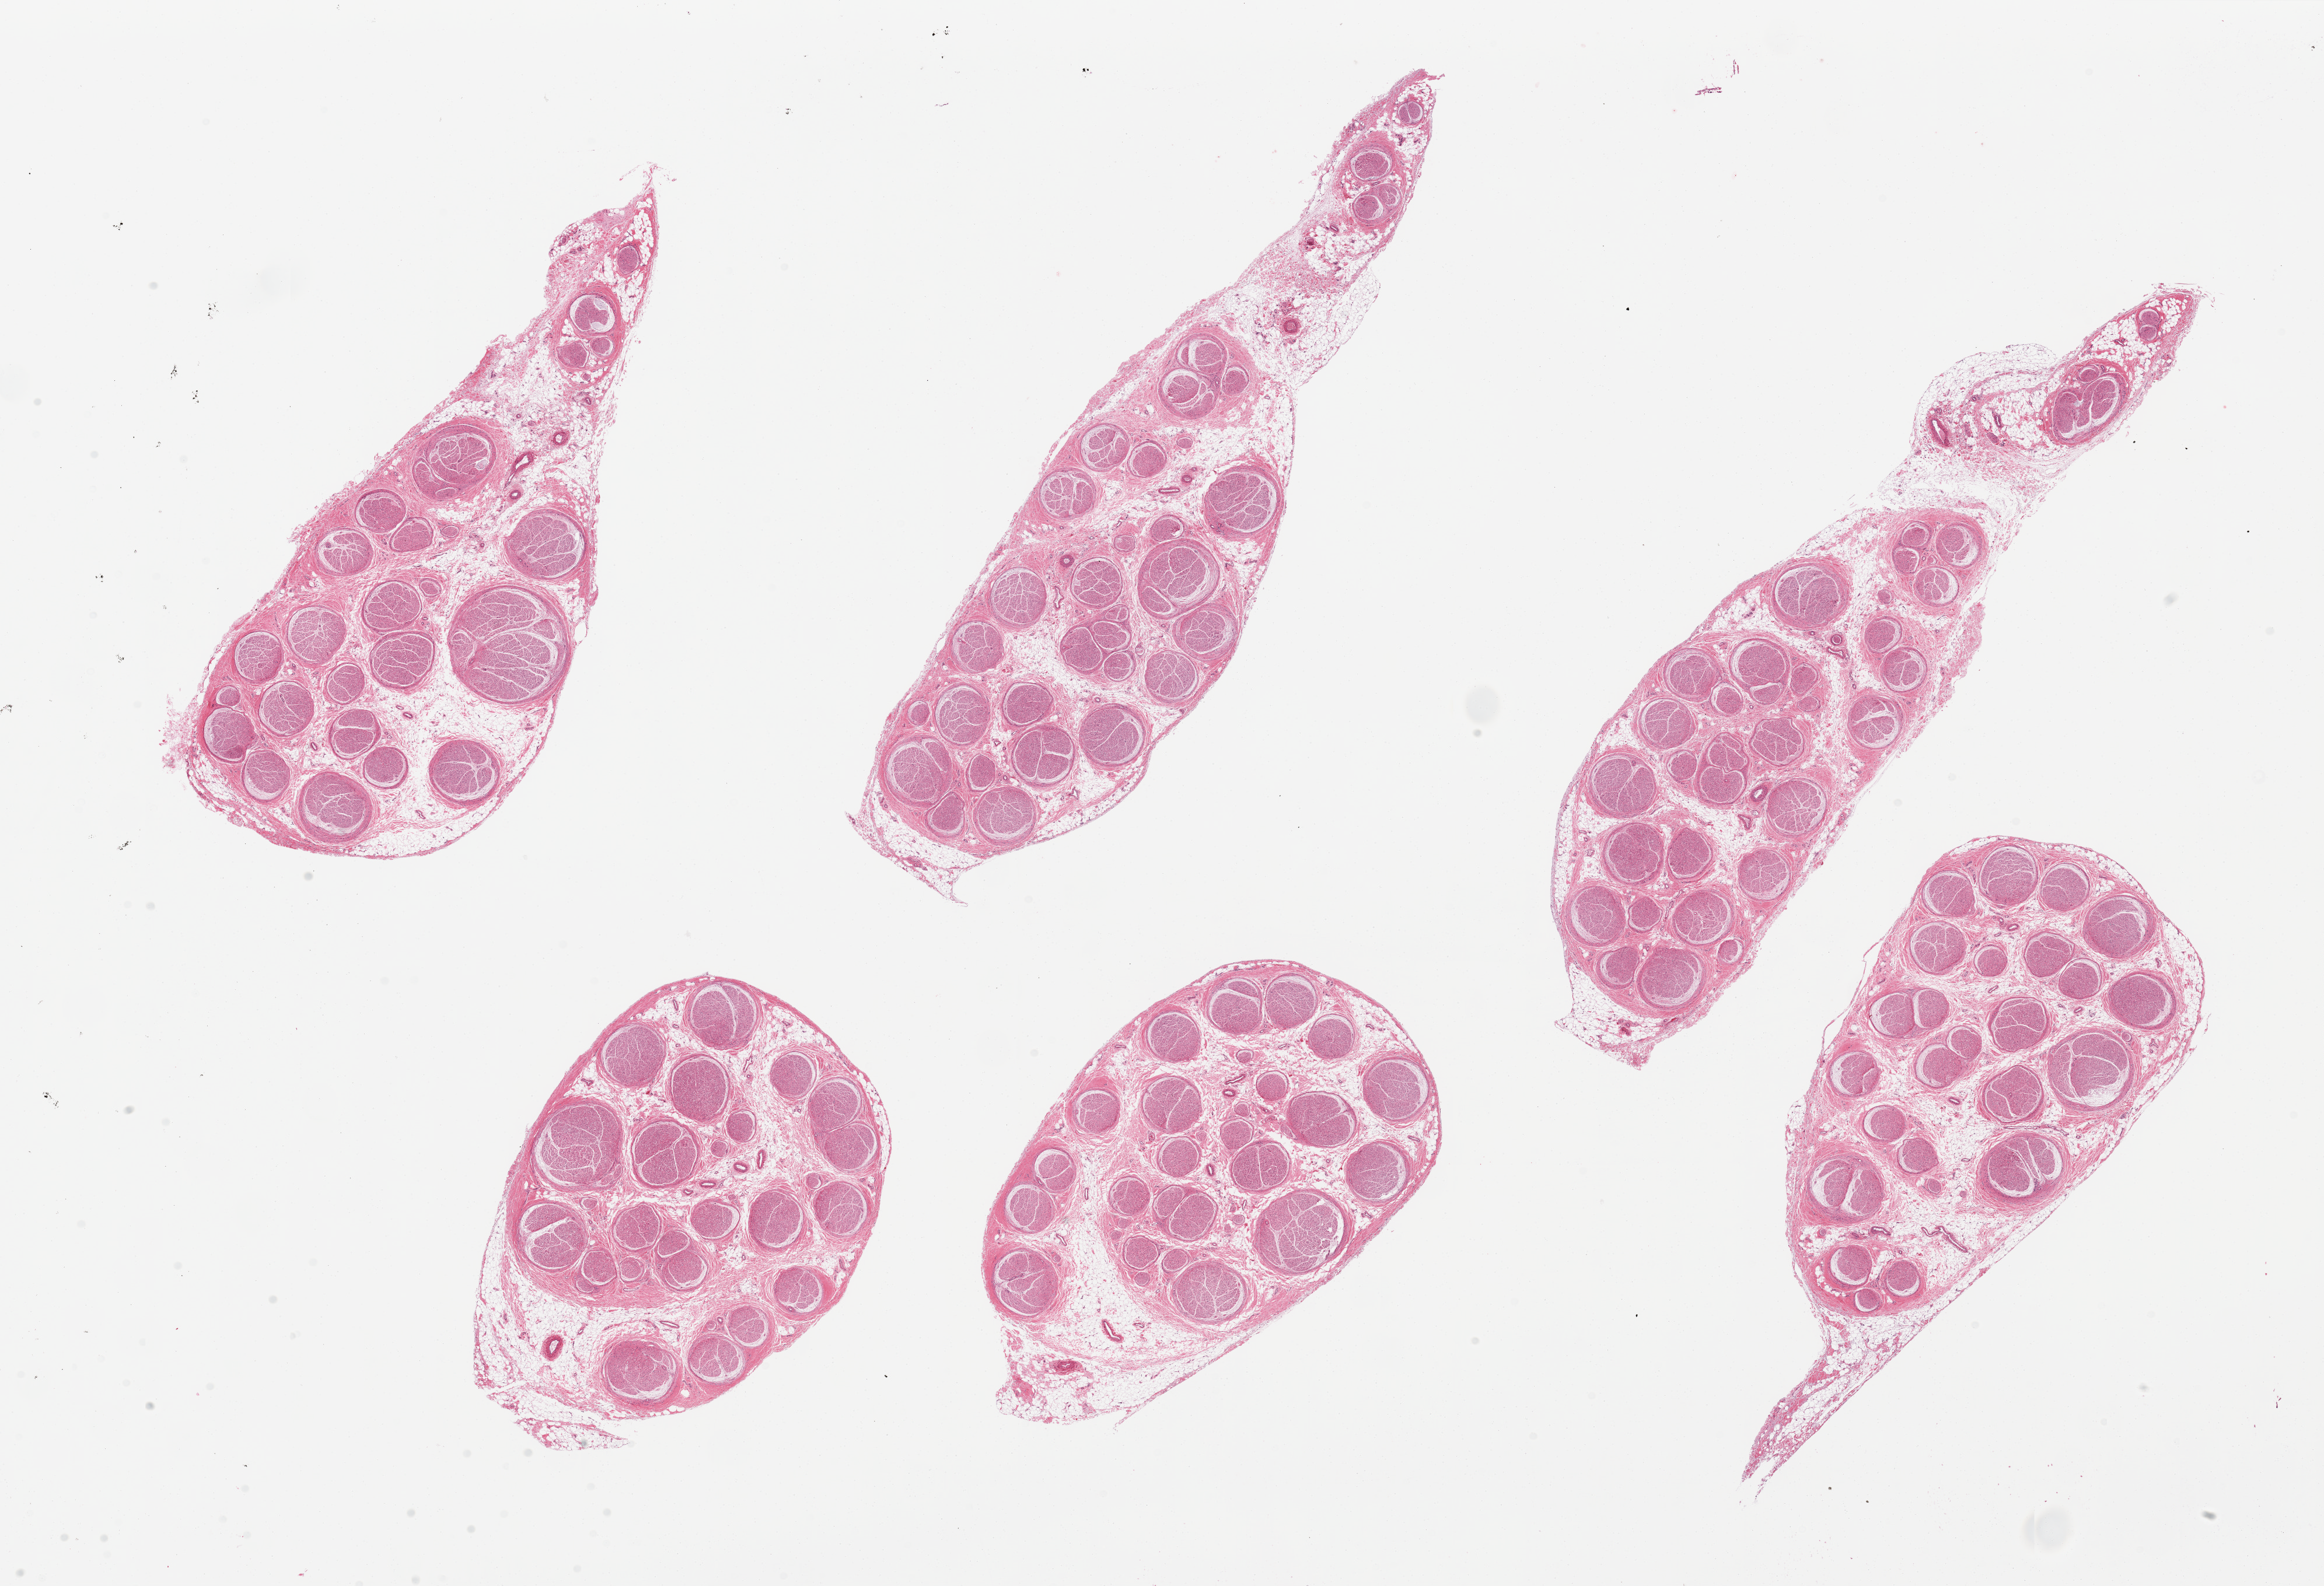
Whole-slide image, haematoxylin and eosin stain, whole scanned area (about 31.5 x 21.5 mm) shown as a low-resolution overview, PAXgene-fixed, paraffin-embedded tissue, target tissue: tibial nerve, tissue donor sample. Male donor.
Review note (as recorded): 6 pieces, includes up to 20-30% fat.